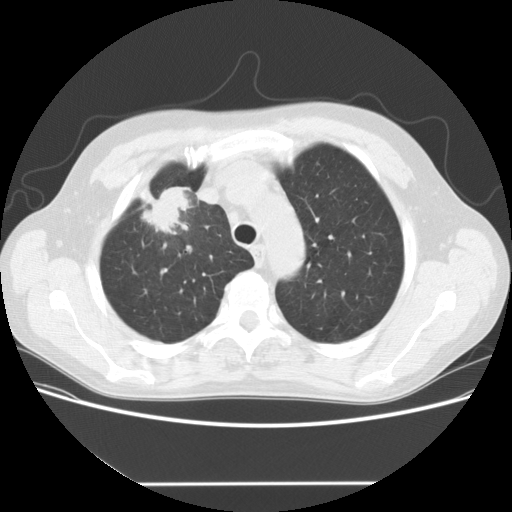
Low-dose screening chest CT, one axial slice. Position 122 of 153 along the scan axis. Reconstruction kernel STANDARD. 120 kVp. Lung window (W 1500 / L -600 HU). 2.5 mm slice thickness. 512 × 512 image matrix.
Outlined on this slice (expert manual segmentation):
- lesion 1 (tumor, upper lobe of right lung): bounding box (x1, y1, x2, y2) in pixels: (139, 187, 192, 234)